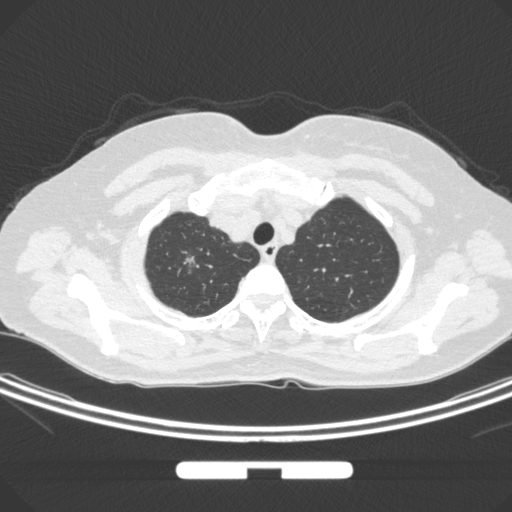
Chest CT, one axial slice; slice 254 of 295 in the series (ordered by position); 120 kVp; lung window (W 1500 / L -600 HU); 1 mm slice thickness; 512 × 512 image matrix, field of view 369 × 369 mm. Female patient, age 58 years. Case-level facts recorded for this patient, not image findings: clinical TNM (as recorded): T1b N0 M0; histopathological grade: G2-3.
Outlined on this slice (bounding box drawn by a radiologist):
- lung tumour (recorded histology: adenocarcinoma): bounding box [x1, y1, x2, y2] px = [178, 250, 202, 277]